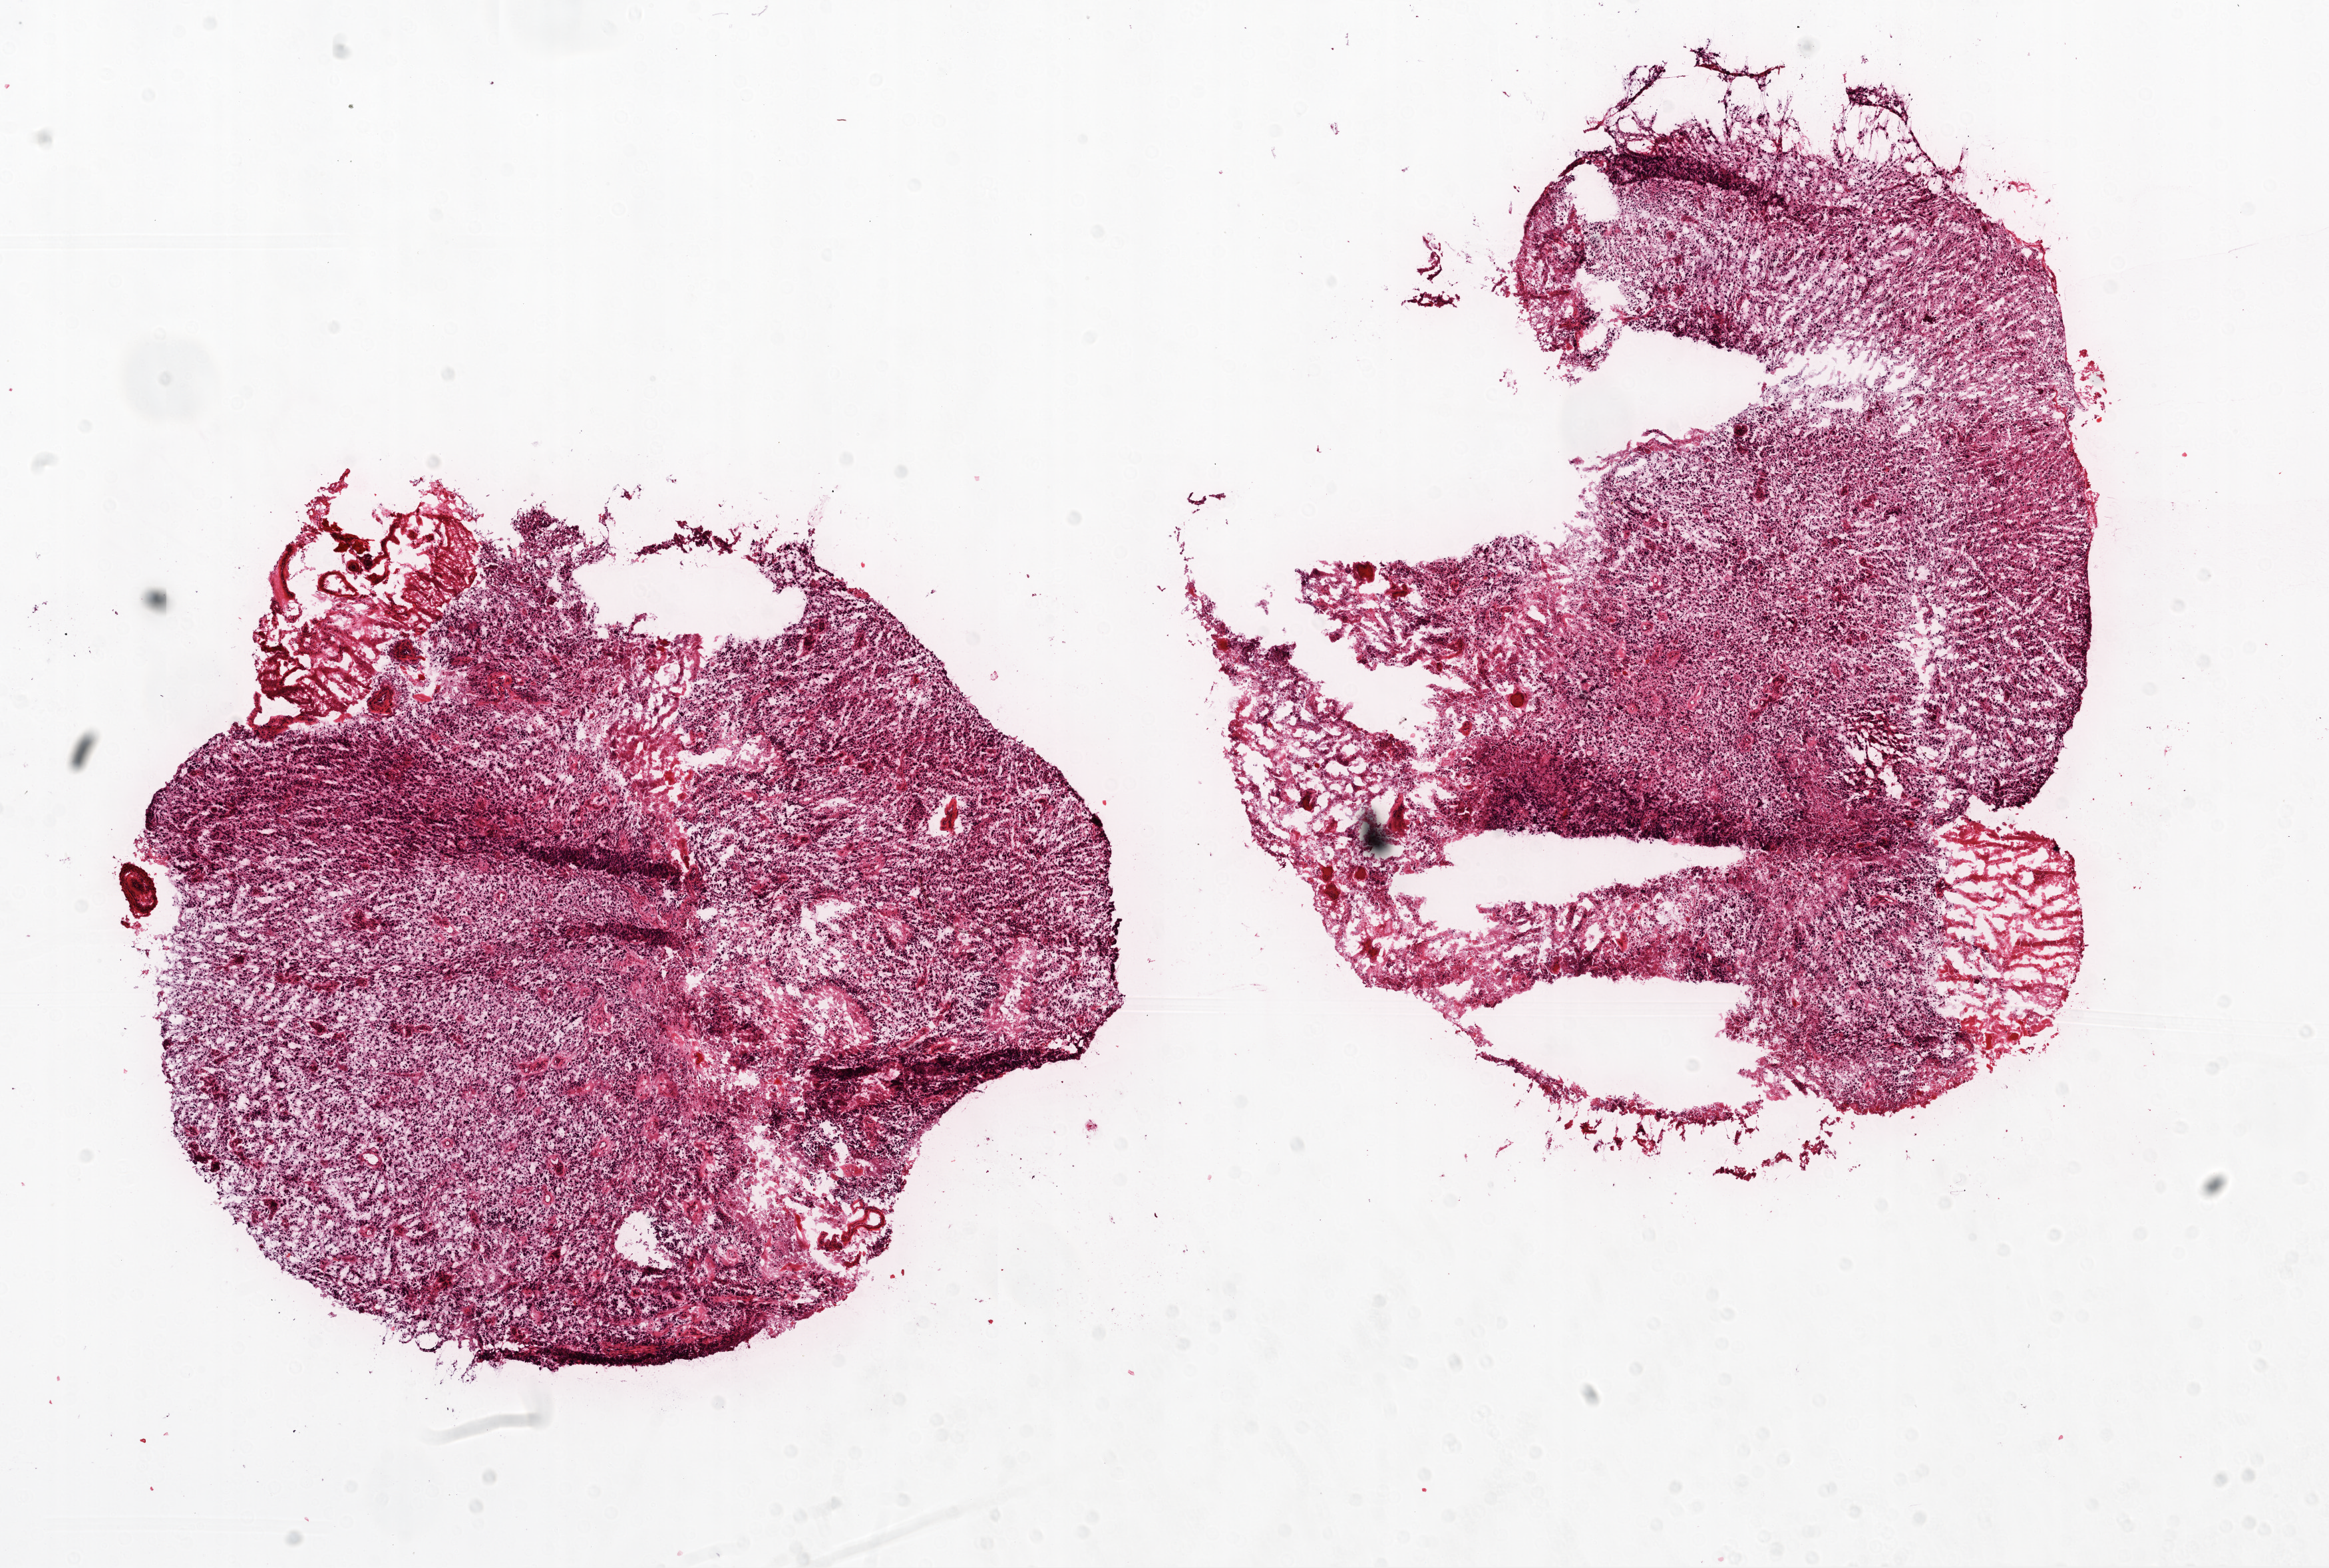
H&E-stained whole-slide image, shown as a low-resolution overview of the whole scanned area (about 14.0 x 9.5 mm); frozen section; sample: primary tumour, brain. Male, age 70 years at initial diagnosis. Slide review estimates, as recorded: tumour cells 83%, tumour nuclei 95%, normal cells 0%, stromal cells 2%, necrosis 15%.
Histologic diagnosis: Glioblastoma.